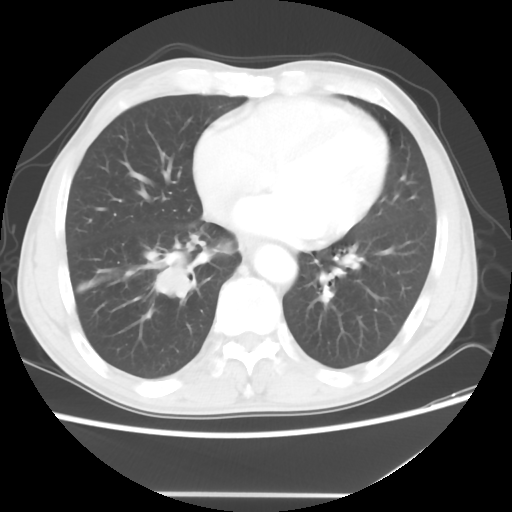
Chest CT, one axial slice; position 18 of 56 along the scan axis; reconstruction kernel STANDARD; 120 kVp; lung window (W 1500 / L -600 HU); 5 mm slice thickness; 512 × 512 image matrix, field of view 344 × 344 mm. Patient: male, 65 years. From the clinical record (not read from this slice): clinical TNM (as recorded): T1c N3 M0.
Outlined on this slice (rectangle marked by the reading radiologist):
- lung tumour (recorded histology: small cell carcinoma): bounding box (x1, y1, x2, y2) in pixels: (148, 251, 202, 305)